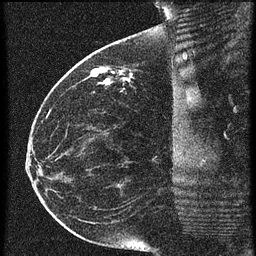
Breast MRI (dynamic contrast-enhanced), one sagittal slice. Slice 25 of 60 in the series (ordered by position). 3 images stored at this slice position (order not interpretable as contrast timing). 1.5 T. TE 4.2 ms, TR 20.4 ms. 1.5 mm slice thickness. 256 × 256 image matrix, field of view 200 × 200 mm. Patient: female, 35 years. From the clinical record (not read from this slice): setting: breast cancer imaged before/during neoadjuvant chemotherapy; receptor status: HR-positive, HER2-negative.
Structures marked on this image (semi-automatically segmented with operator editing):
- analysis volume of interest (the breast-tissue region the enhancement analysis was run in; not a lesion): bounding box [x1, y1, x2, y2] px = [84, 50, 179, 97]
- tumour enhancement mask (voxels above the 90 % enhancement threshold inside the analysis volume of interest): [92, 68, 121, 85]